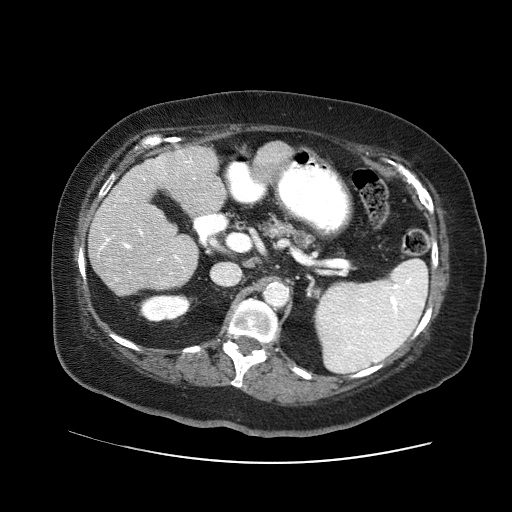
Contrast-enhanced abdominal CT (liver protocol), one axial slice; position 22 of 71 along the scan axis; reconstruction kernel STANDARD; 120 kVp; soft-tissue window (W 400 / L 40 HU); 512 × 512 image matrix, field of view 400 × 400 mm. Case-level facts recorded for this patient, not image findings: diagnosis: hepatocellular carcinoma (patient treated with transarterial chemoembolisation; whether this scan precedes or follows treatment is not stated here); TNM stage (as recorded): Stage-II; Child-Pugh class: A; tumour size: 5 cm.
Annotated regions visible in this slice (semi-automatically segmented with operator editing):
- liver parenchyma outside the tumour (the mass and vessels are separate outlines, so this box may not span the whole liver): box from (x=88, y=142) to (x=292, y=294) px
- liver vessels: (x=100, y=152)–(x=192, y=280)